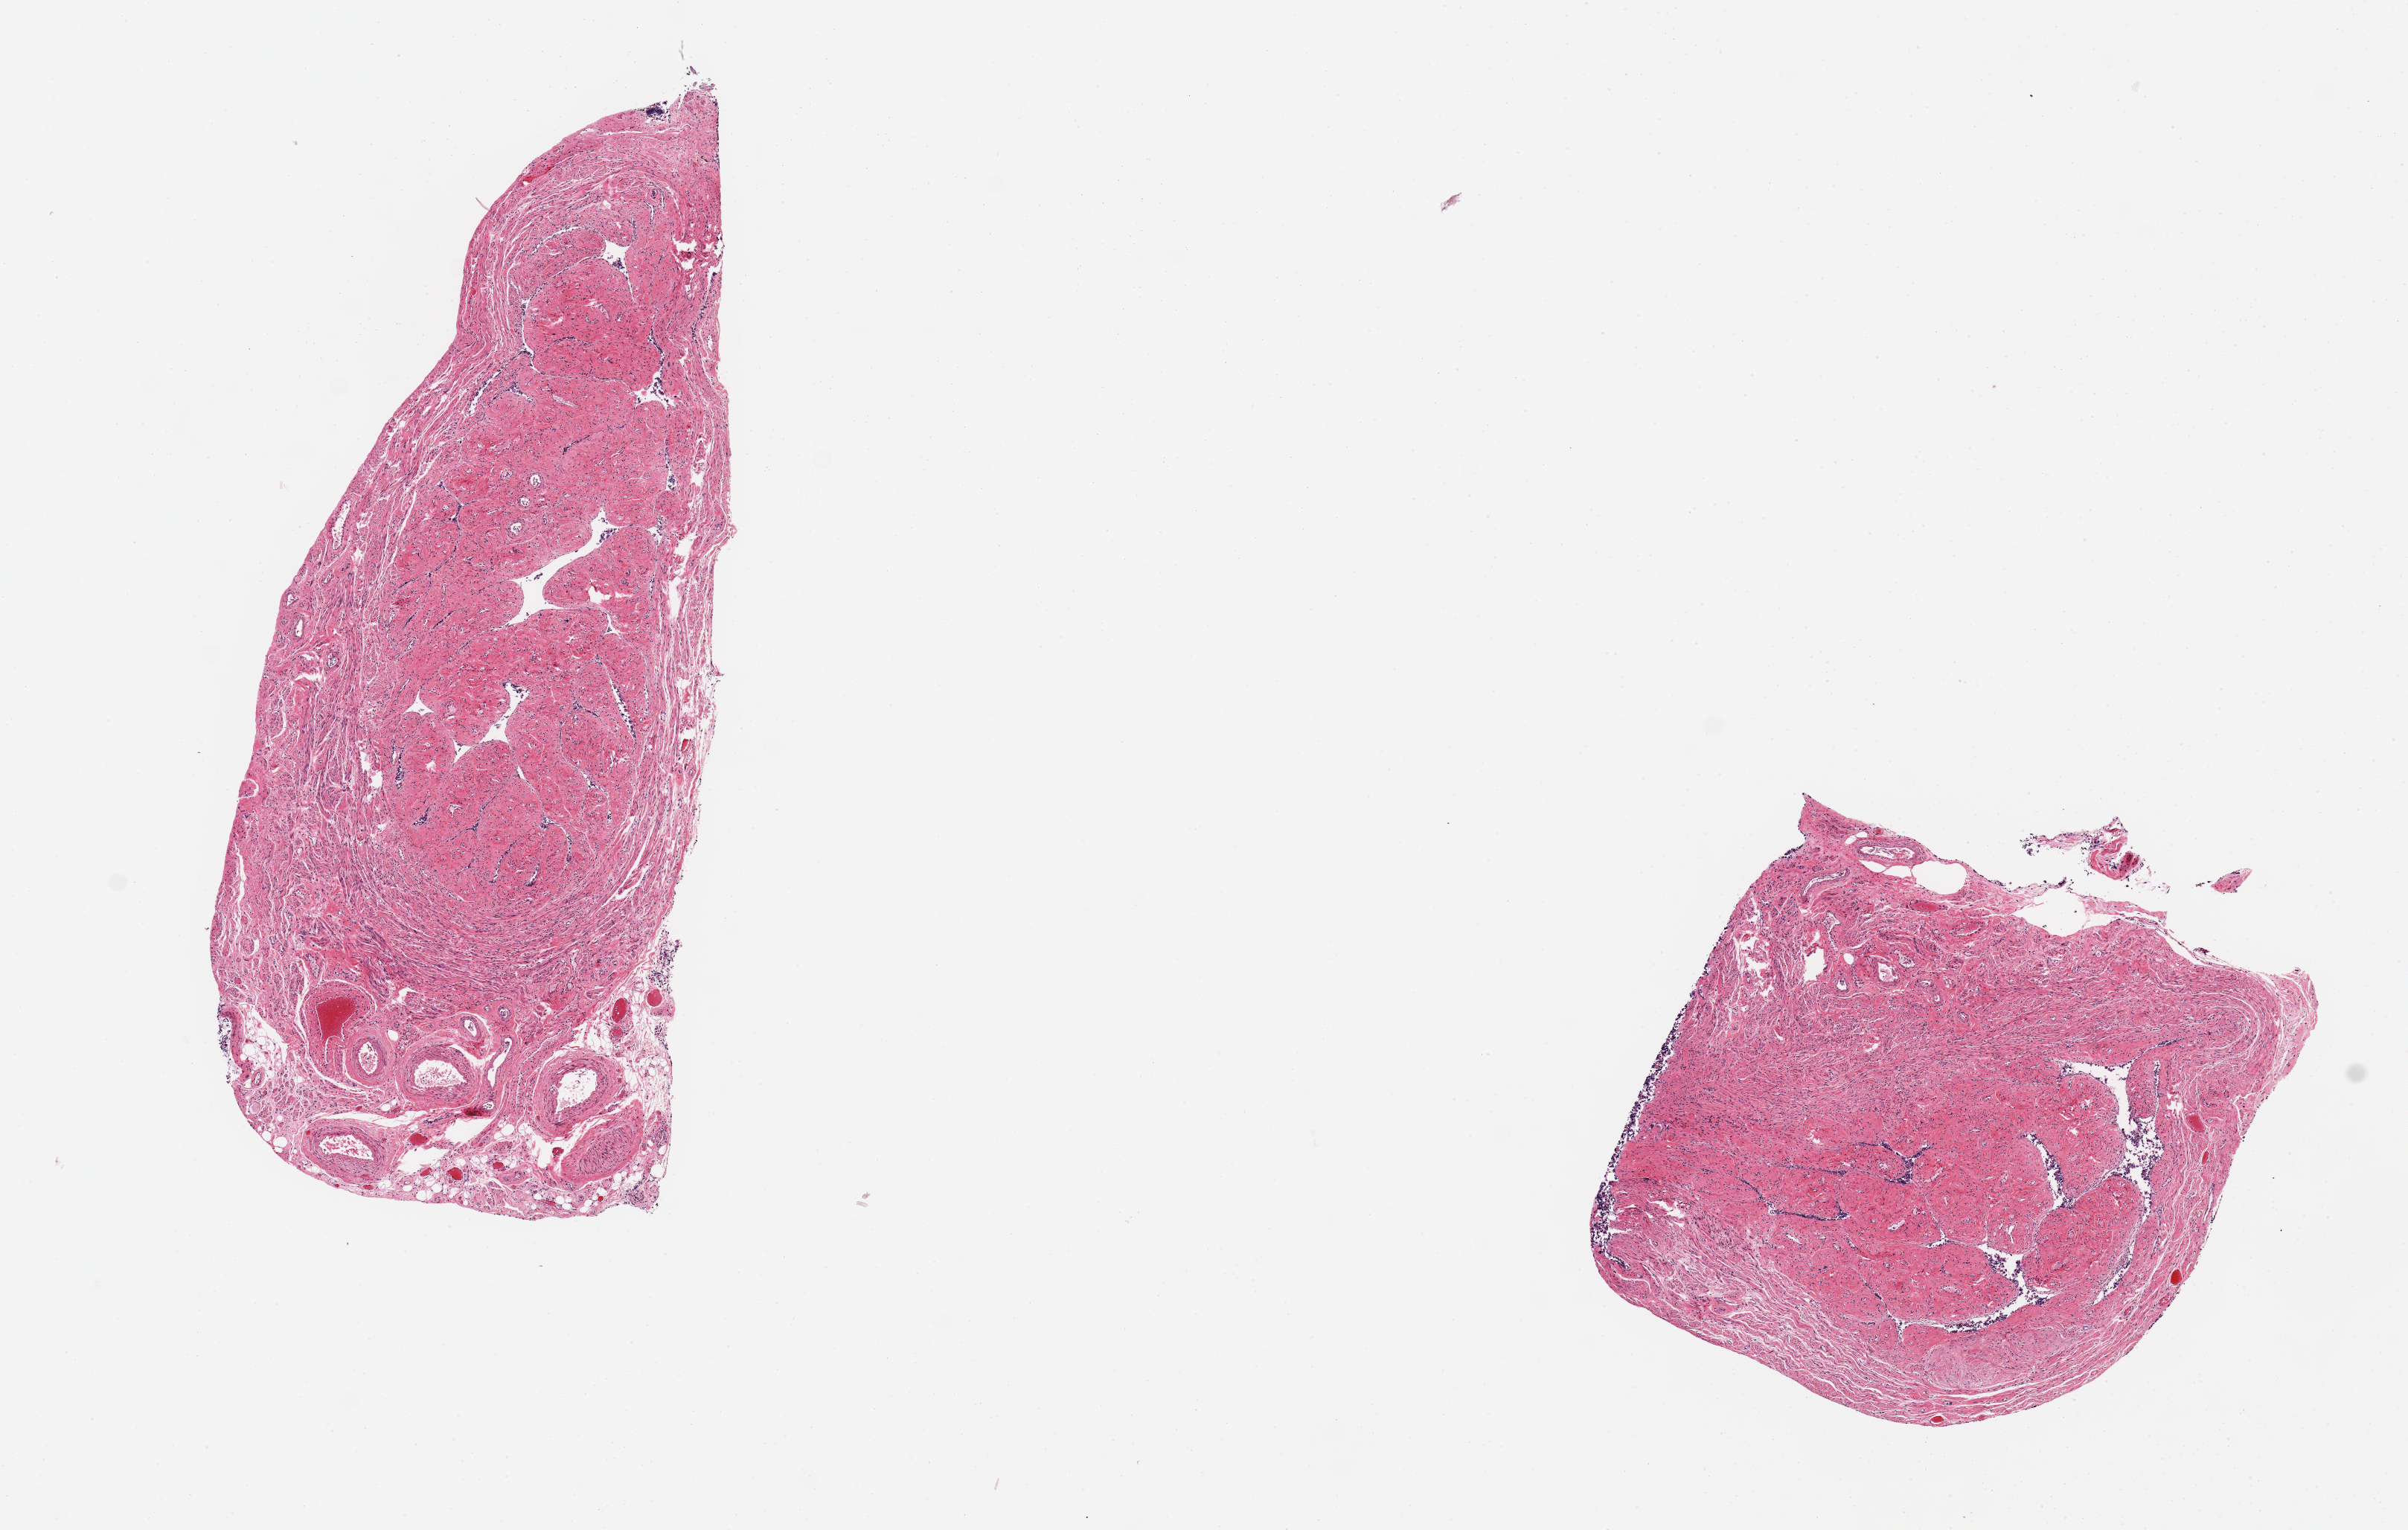
Hematoxylin and eosin (H&E) whole-slide image — whole scanned area (about 12.8 x 8.1 mm) shown as a low-resolution overview. PAXgene-fixed paraffin-embedded (PFPE) section. Sampled site (target tissue): fallopian tube. Donor tissue sample.
Pathologist's review note for this sample: 2 pieces, 6x2 & 3x3 mm; mucosa almost completely sloughed, wall slight to moderate autolysis.